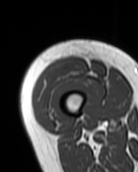
MRI of an extremity soft-tissue mass, one axial slice; position 15 of 99 along the scan axis; MR volume resampled by the dataset authors to the PET/CT grid (not the native acquisition matrix); 138 × 172 image matrix, field of view 135 × 168 mm. Female patient. From the clinical record (not read from this slice): histological type: pleiomorphic undifferentiated sarcoma; grade: high; site of the primary tumour: right quadricep.
Outlined on this slice (expert contour drawn on MRI and transferred to this co-registered scan by the dataset authors):
- gross tumour volume including surrounding oedema: bounding box <34,59,88,113> (left, top, right, bottom; pixels)